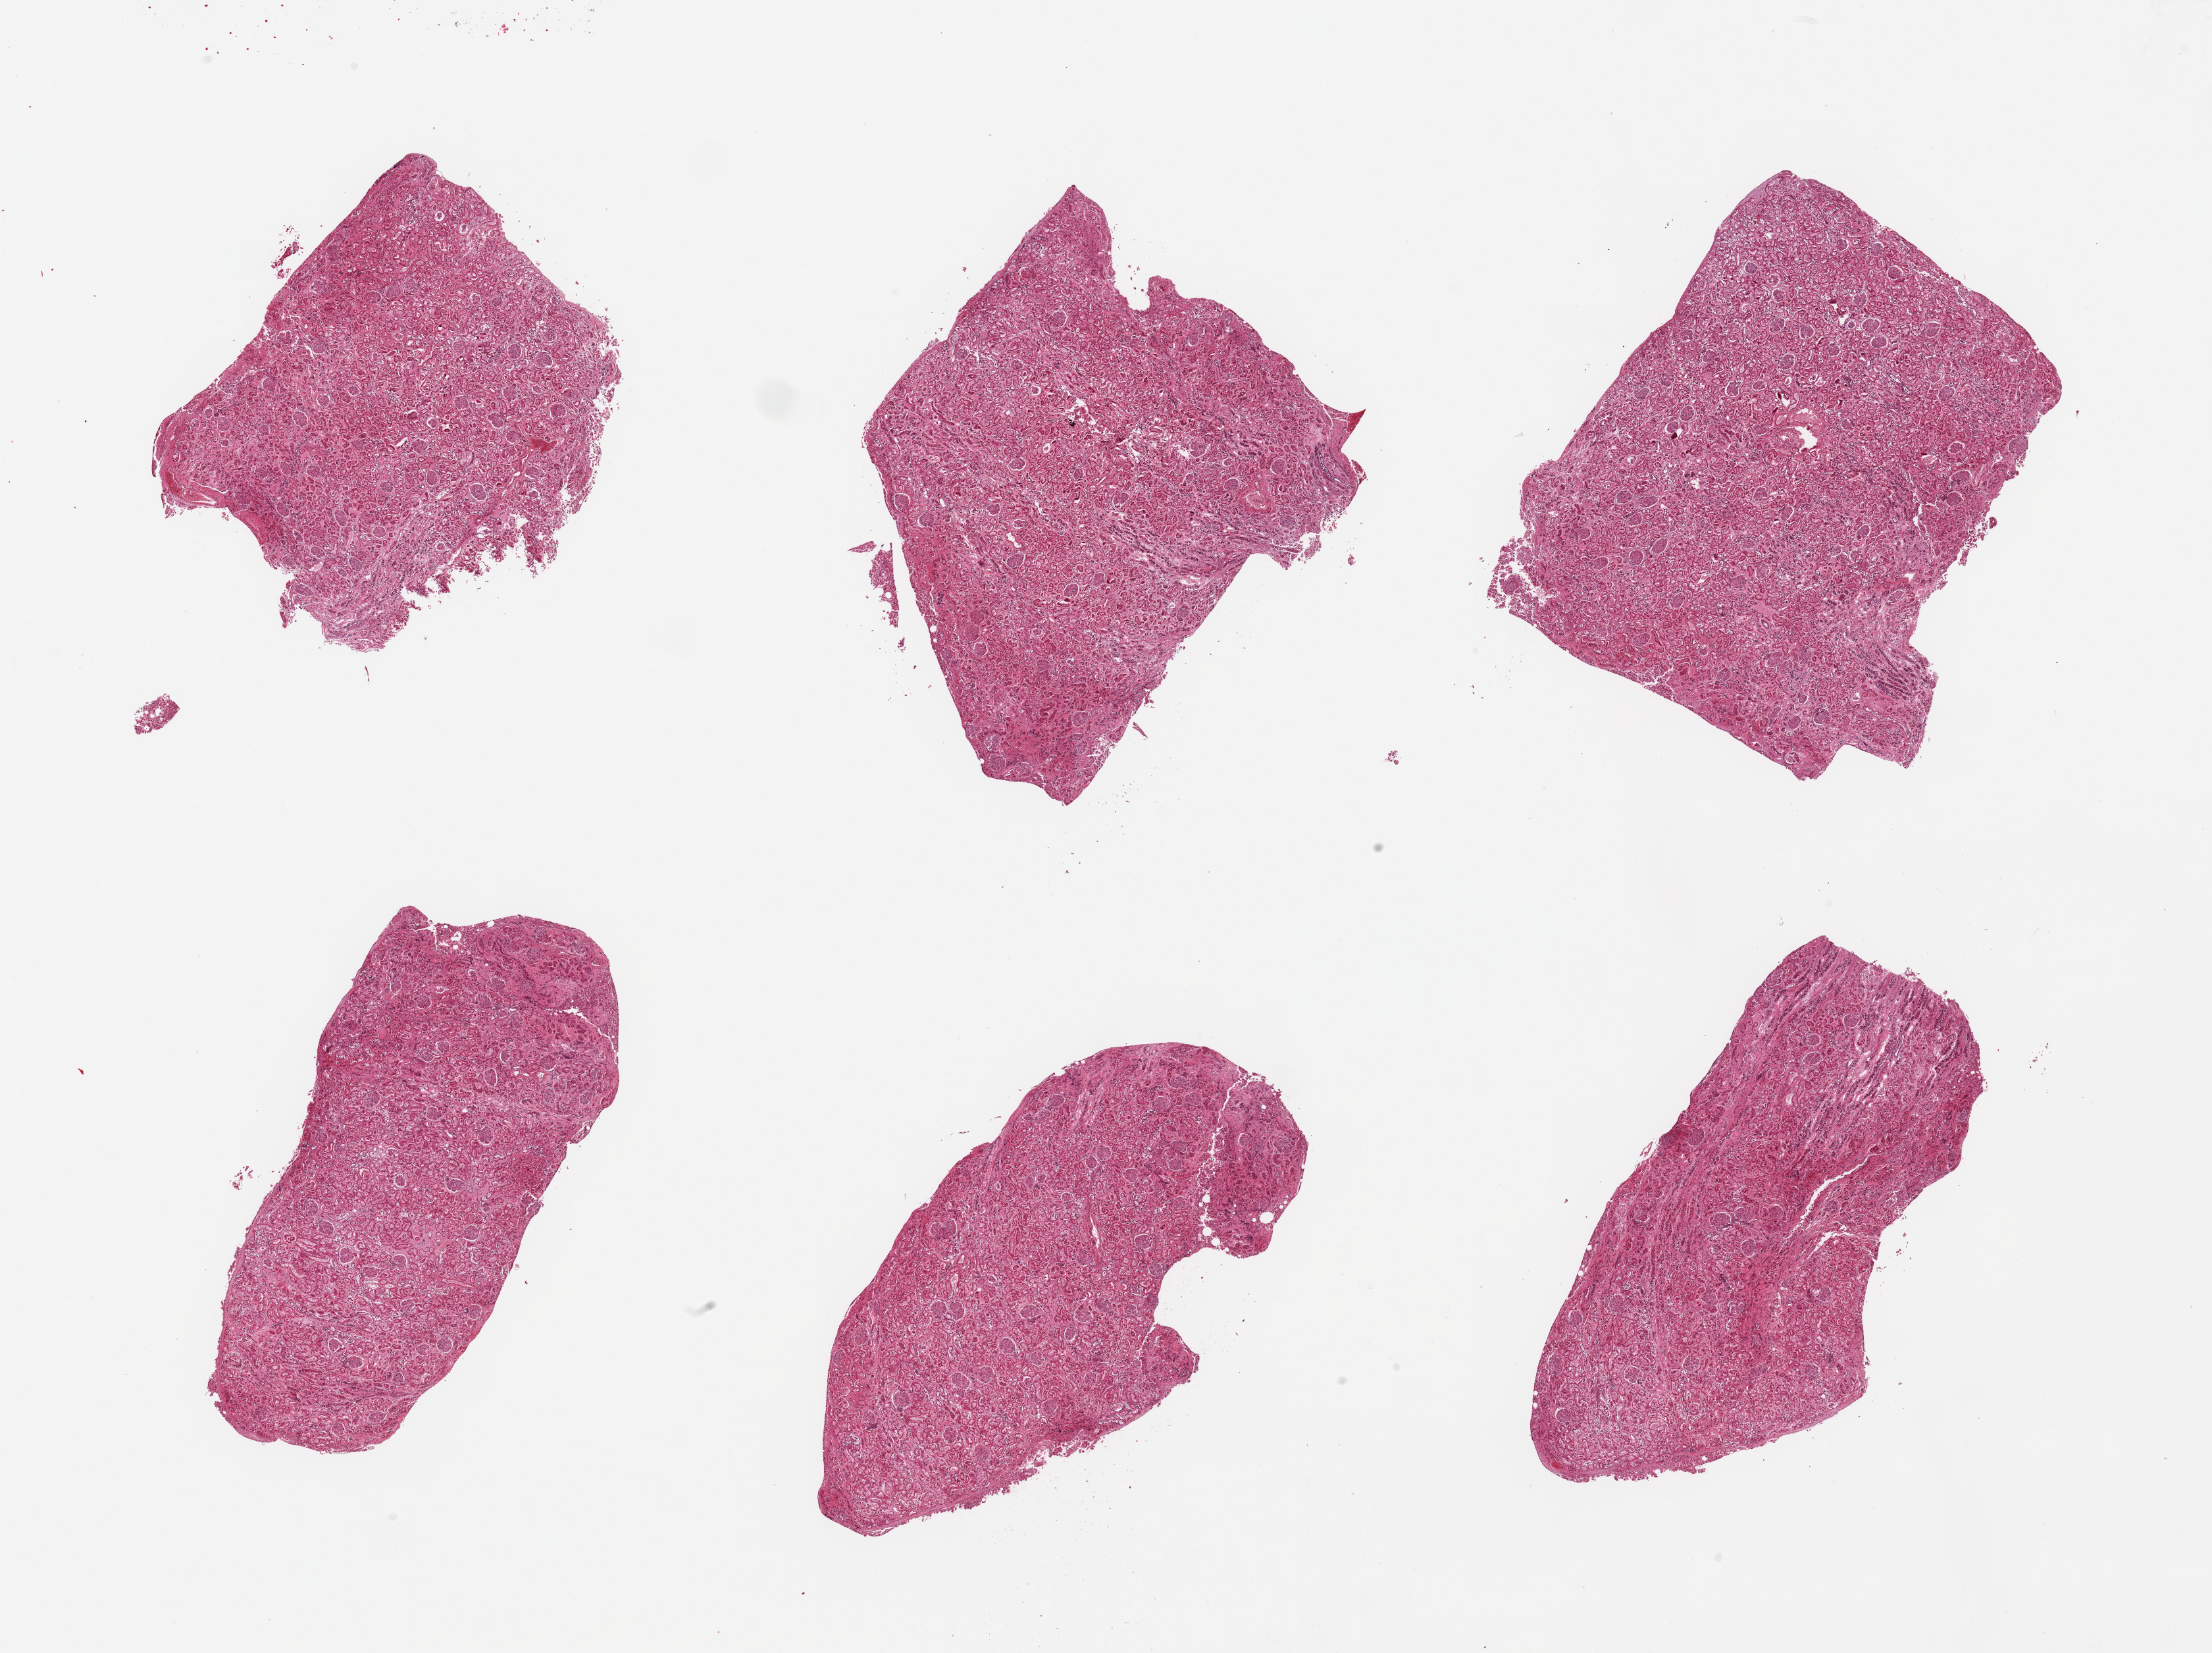
Digitized hematoxylin and eosin (H&E)-stained section — a low-resolution overview of the entire scanned area, about 26.6 x 19.9 mm. PAXgene-fixed, paraffin-embedded tissue. Sampled site (target tissue): renal cortex. Tissue donor sample. Donor: male.
* reviewer comment on this tissue sample: 6 pieces; glomeruli in all sections, some interstitial fibrosis